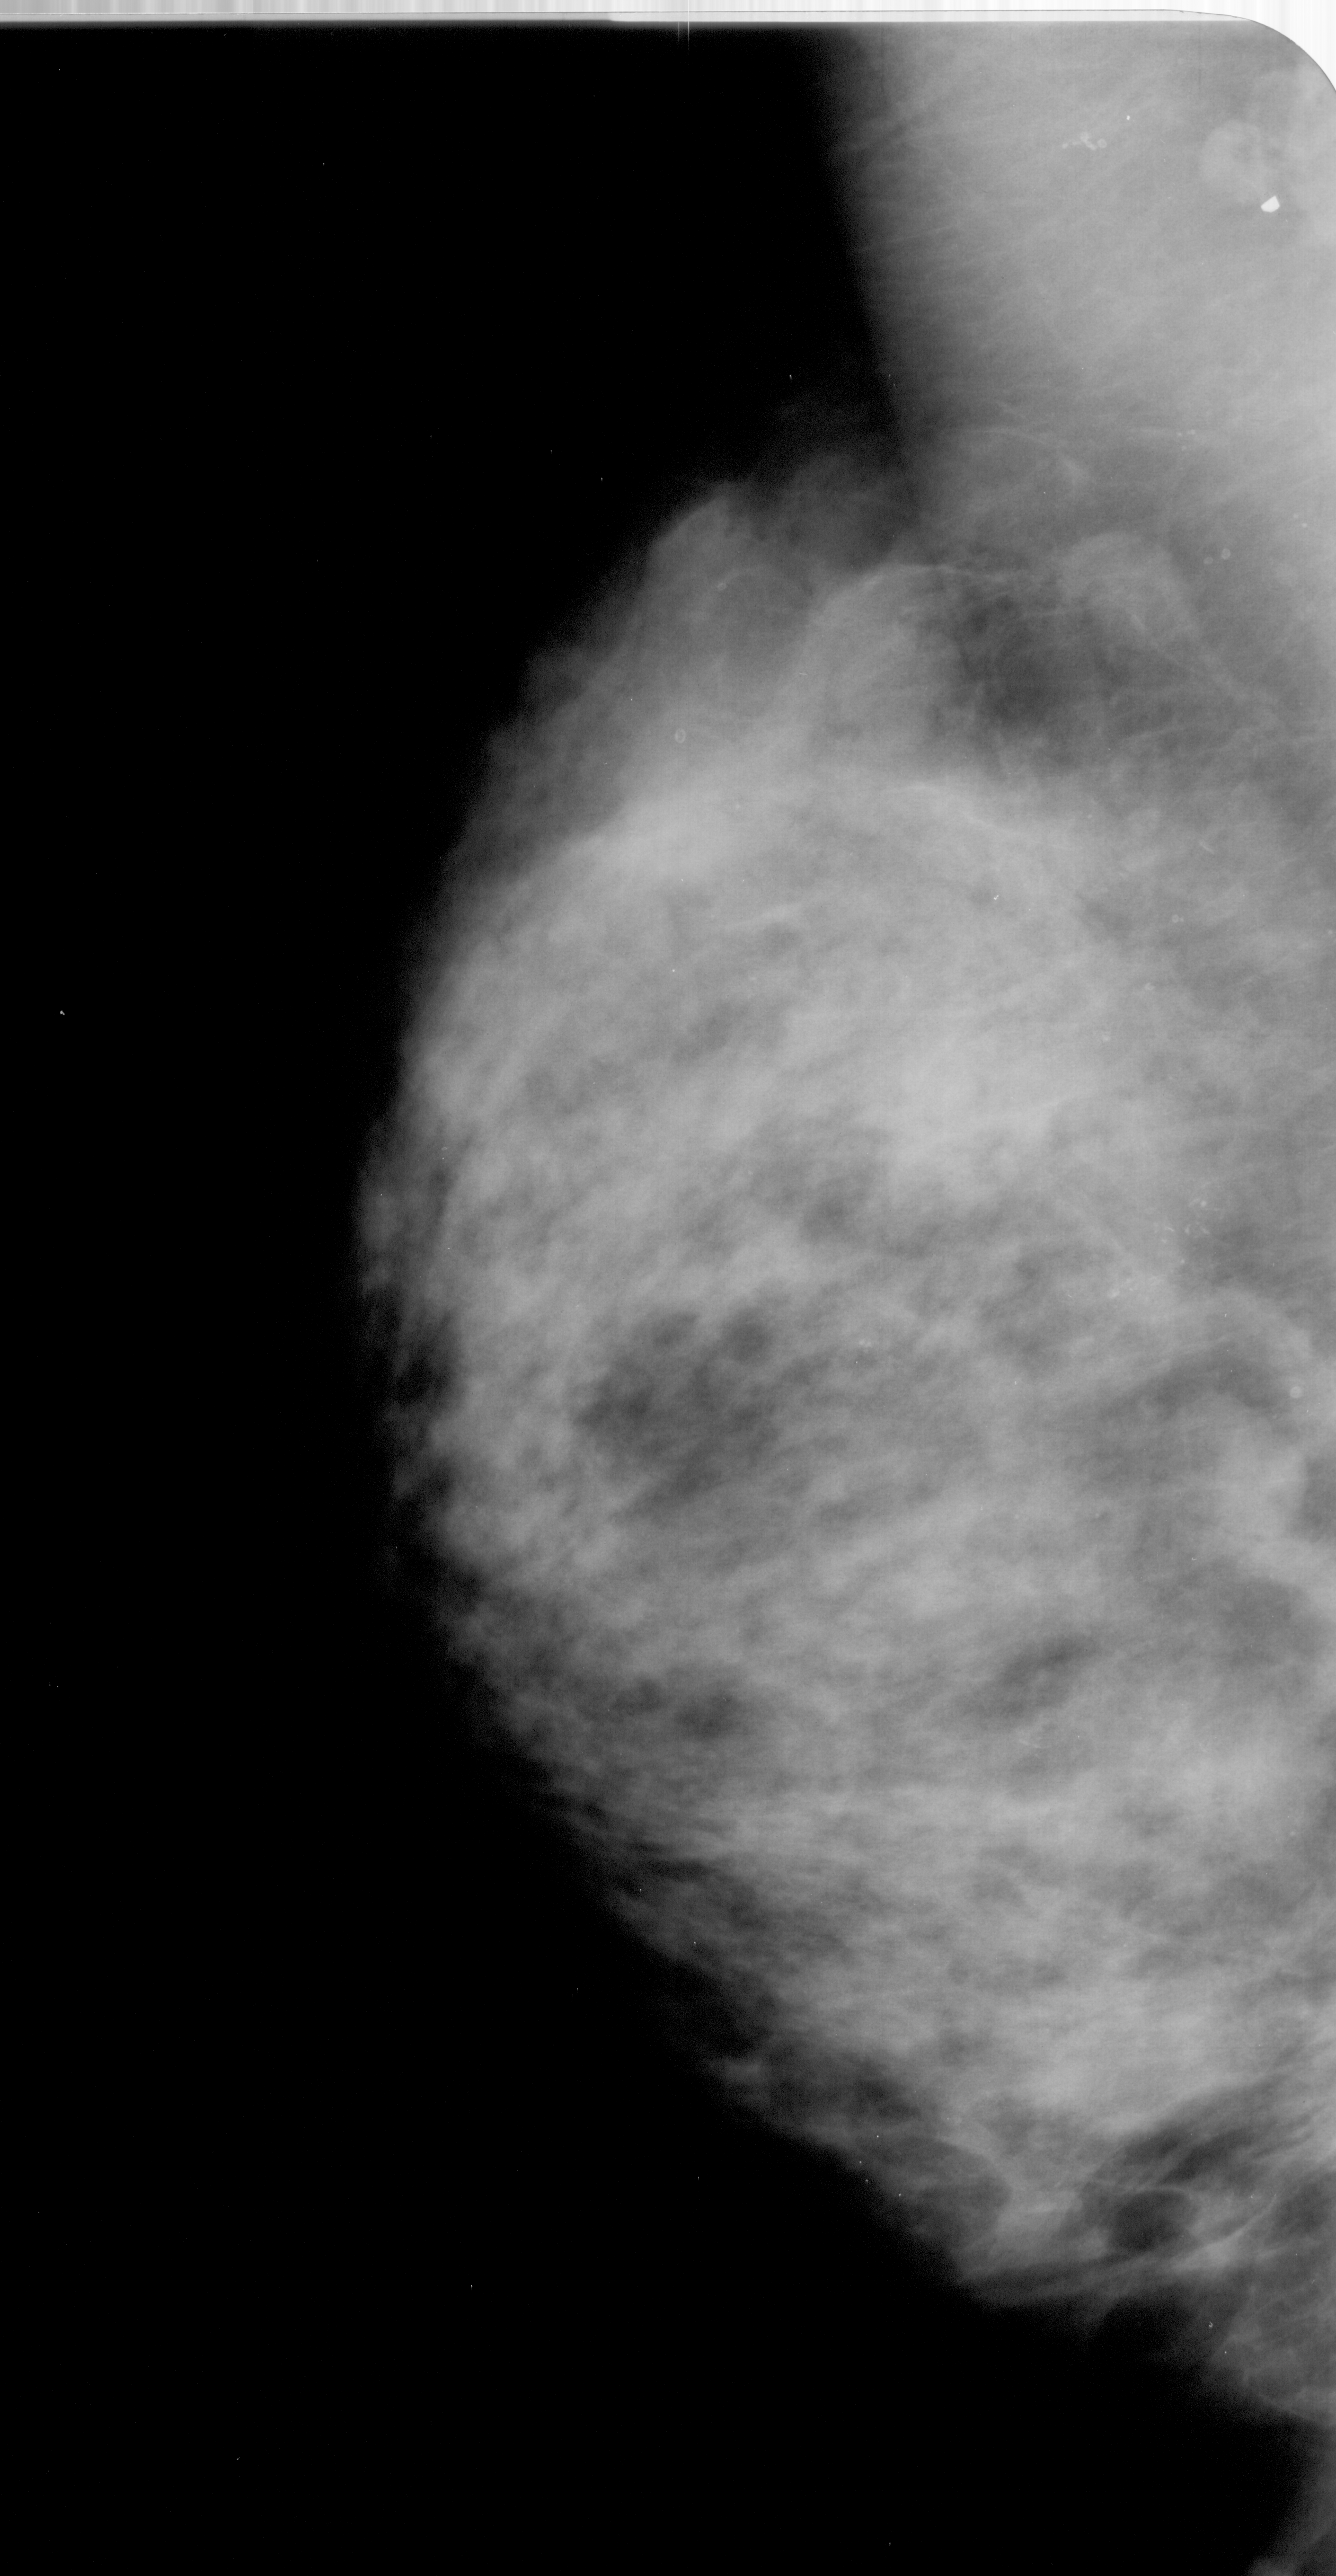
Mammogram (digitized film); left breast; MLO view; breast composition: heterogeneously dense (BI-RADS density category 3 of 4).
Marked findings (only marked abnormalities are described; nothing is implied about the rest of the image): calcifications, morphology pleomorphic, distribution clustered; BI-RADS assessment category 4; subtlety rating 2 on a 1 (subtle) to 5 (obvious) scale; pathology (as recorded): malignant.